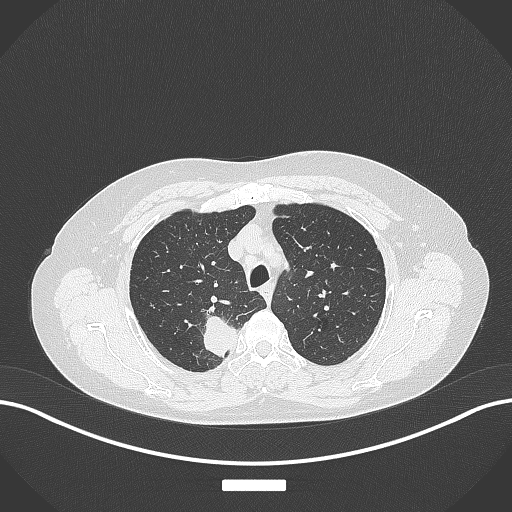
Chest CT, one axial slice. Position 305 of 357 along the scan axis. Lung window (W 1500 / L -600 HU). 512 × 512 image matrix, field of view 400 × 400 mm. Patient: female, 62 years. From the clinical record (not read from this slice): clinical TNM (as recorded): T1c N1 M0.
Annotated regions visible in this slice (rectangle marked by the reading radiologist):
- lung tumour (recorded histology: squamous cell carcinoma): box from (x=198, y=308) to (x=234, y=360) px